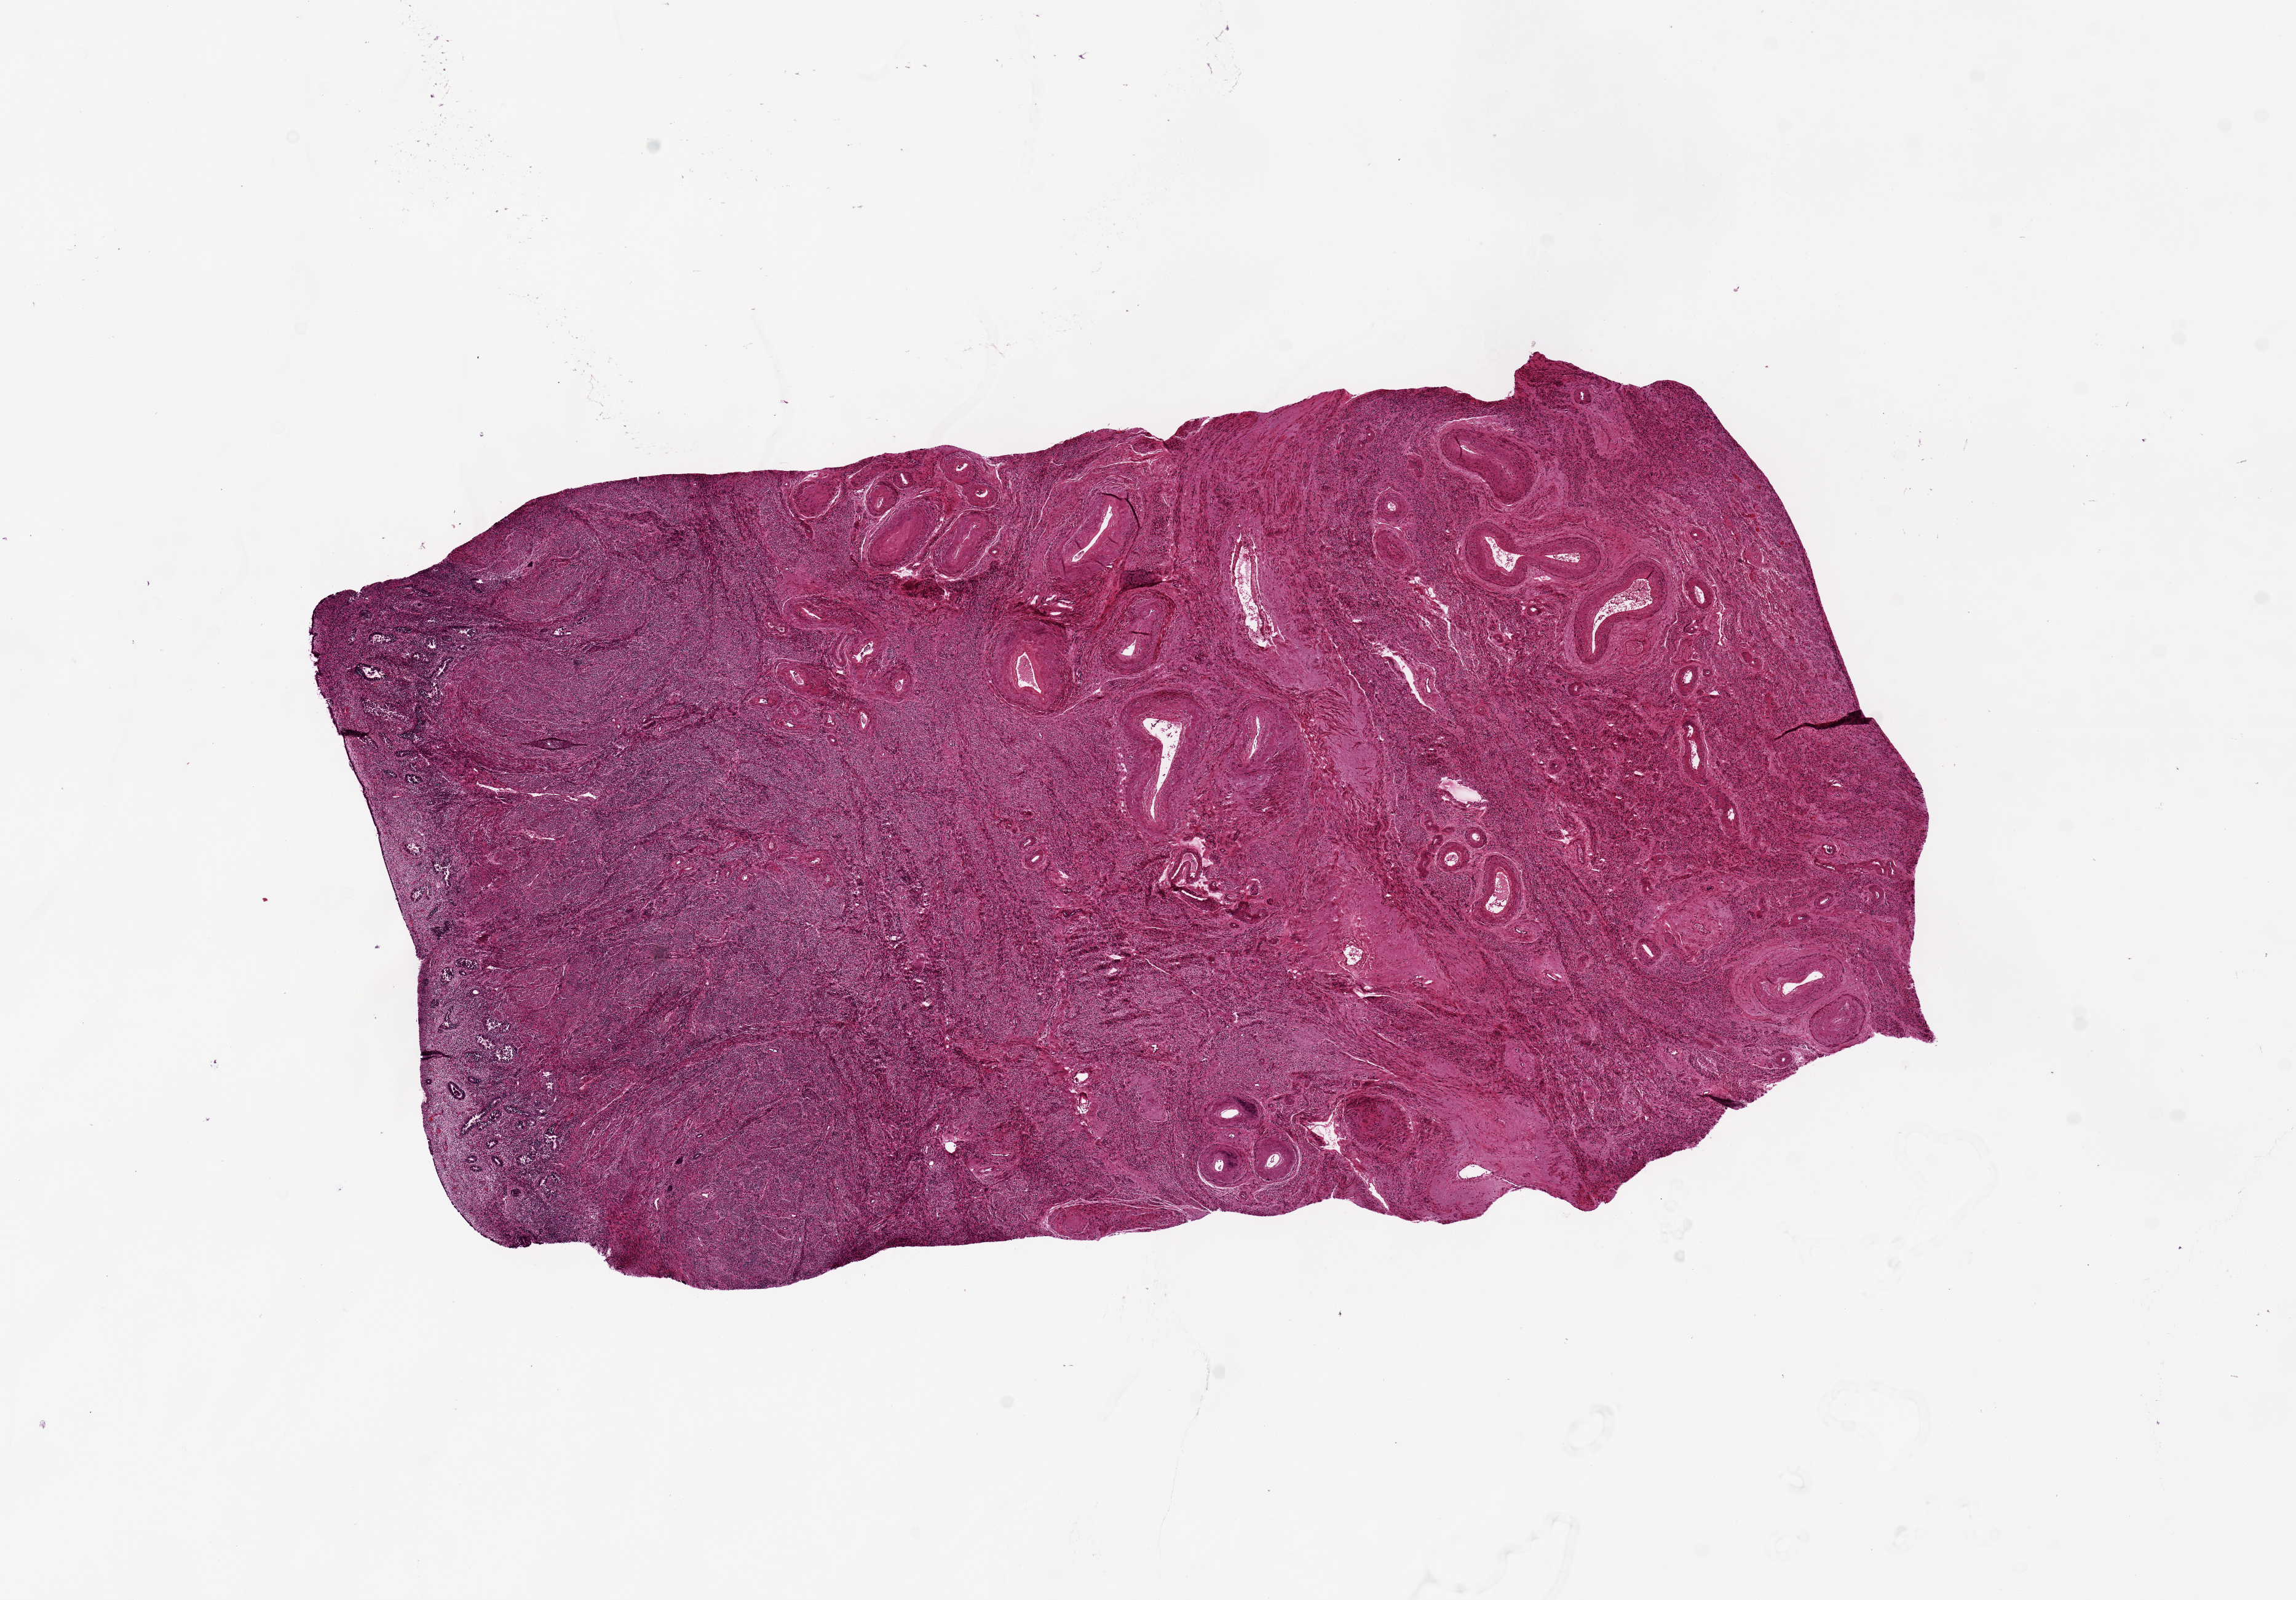
Whole-slide image, H&E stain, brightfield — low-resolution overview of the scanned area, about 14.8 x 10.3 mm (acquisition: 20x scan), PAXgene-fixed, paraffin-embedded tissue, sampled site (target tissue): uterus, tissue donor sample. Donor: female.
Review note (as recorded): Basalis endometrium <5% of specimen. Endometrium moderately autolyzed.